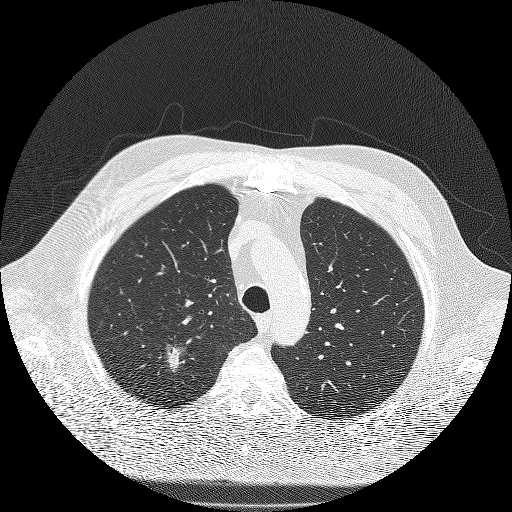
Chest CT (low-dose screening protocol), one axial image. Second annual screen. Lung window (W 1500 / L -600 HU). Male participant, aged 71 years at enrolment. Former smoker at enrolment.
- Expert reader's lesion annotation, bounding box (x1, y1, x2, y2) in pixels: (140, 328, 202, 389).
- The screening reader recorded 3 non-calcified nodules or masses ≥4 mm on this exam (right upper lobe, right upper lobe, right lower lobe); which of them this box marks is not recorded.
- Official screen result: positive, other.
- Later outcome: lung cancer diagnosed 59 days after this screen — bronchiolo-alveolar adenocarcinoma, NOS, right upper lobe, moderately differentiated (G2), stage IIIA (AJCC 6th edition), 25 mm at pathology.